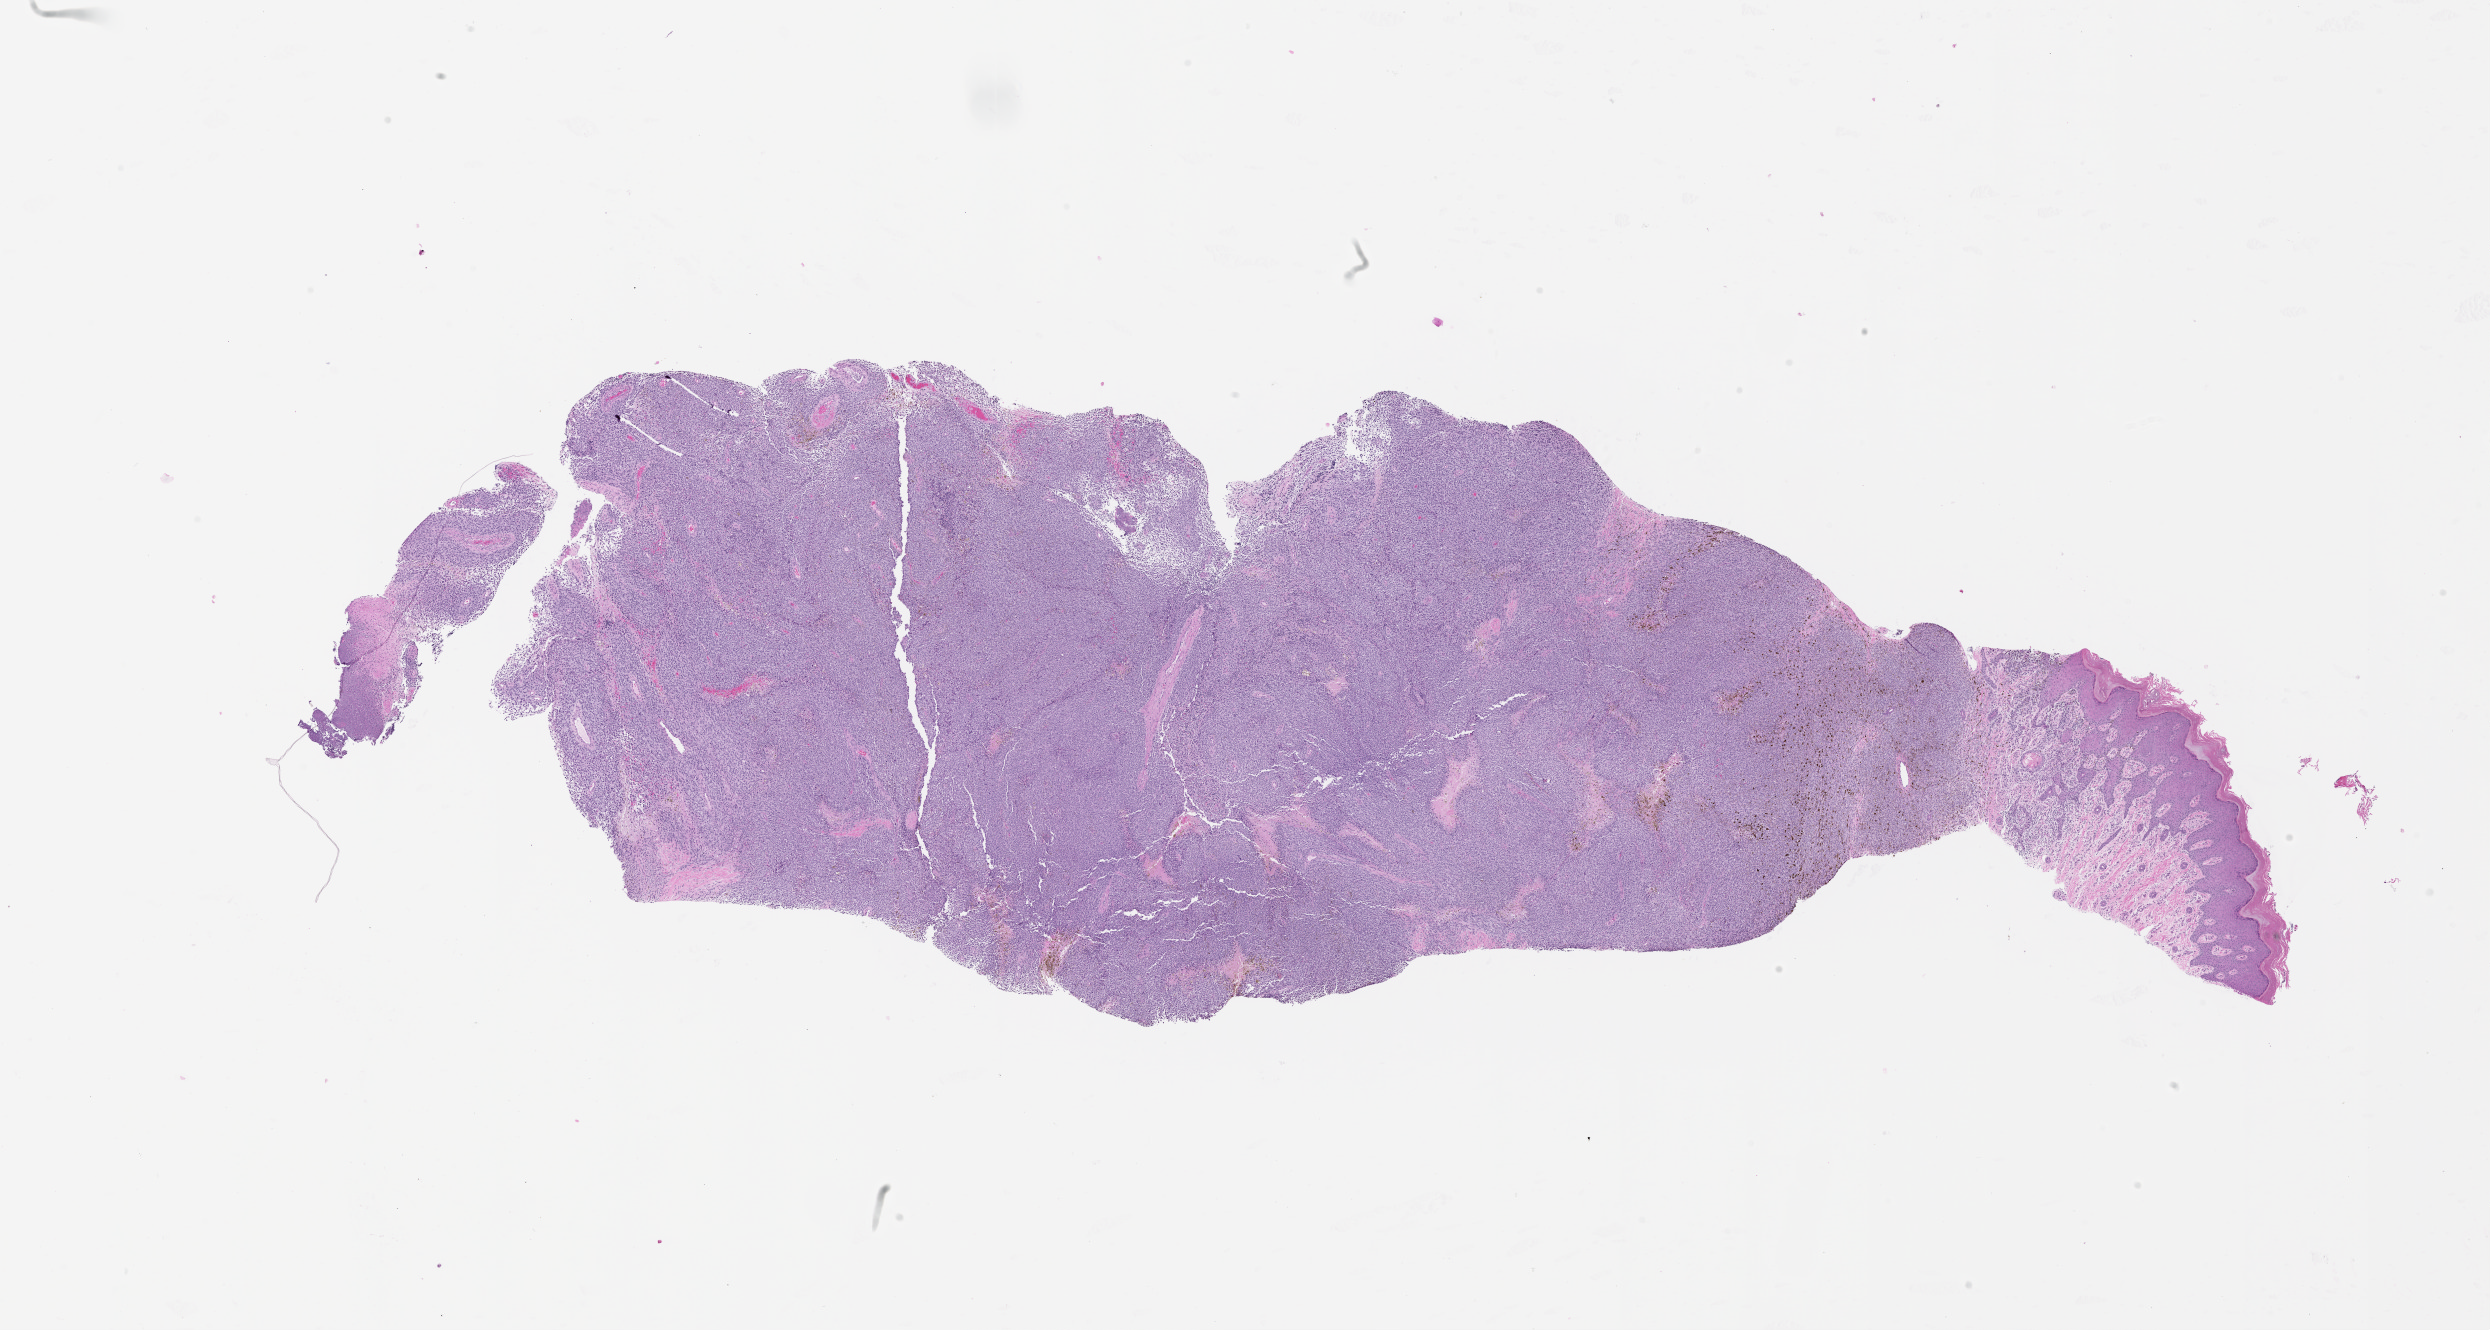
Whole-slide histology image, Hematoxylin and eosin (H&E) stained — low-resolution overview of the scanned area, about 20.0 x 10.7 mm (from a 20x scan); tumour tissue sample, sampled site: skin. 64-year-old male patient. Pathologist review of this section (percent, as recorded): tumour nuclei 80%, necrosis 0%.
- AJCC pathologic stage: IIIC
- histologic diagnosis: Malignant melanoma, NOS